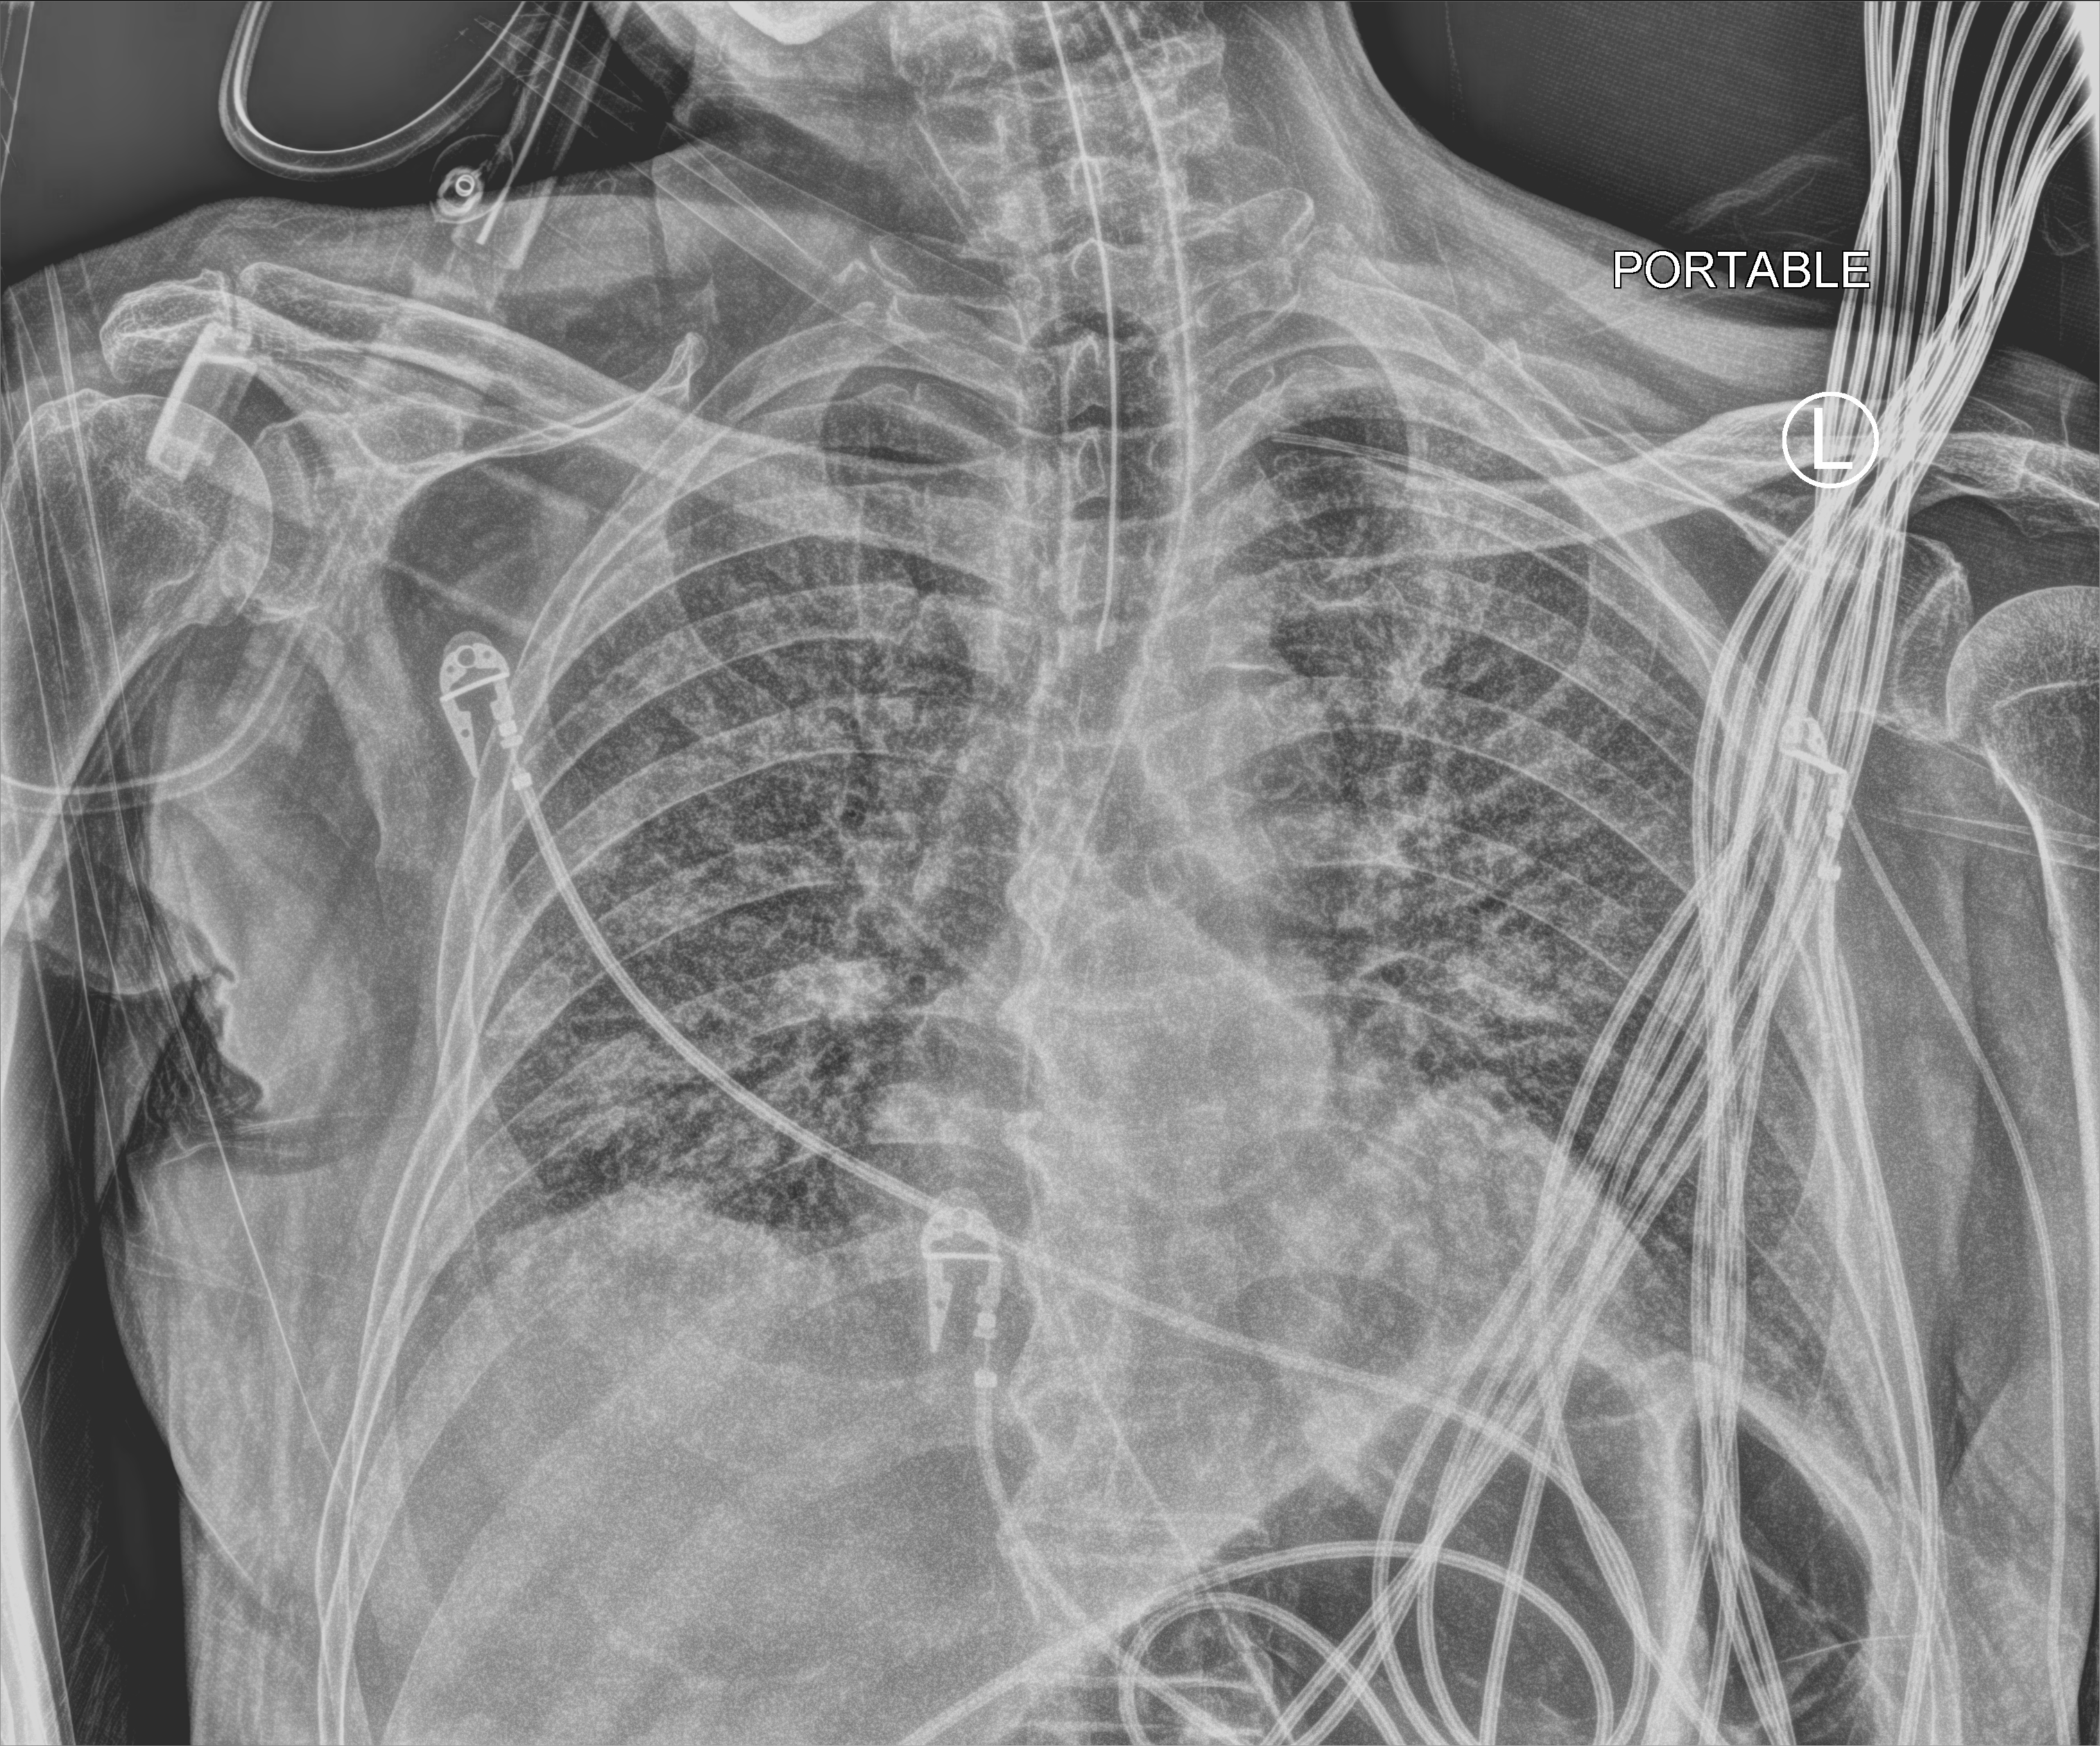
Portable chest radiograph; anteroposterior (AP) projection. Patient hospitalised with COVID-19; male, aged 75–90 years.
Admission-level facts for this patient (not findings on this image; timing relative to this image not recorded): admitted to intensive care during this hospital stay: yes.